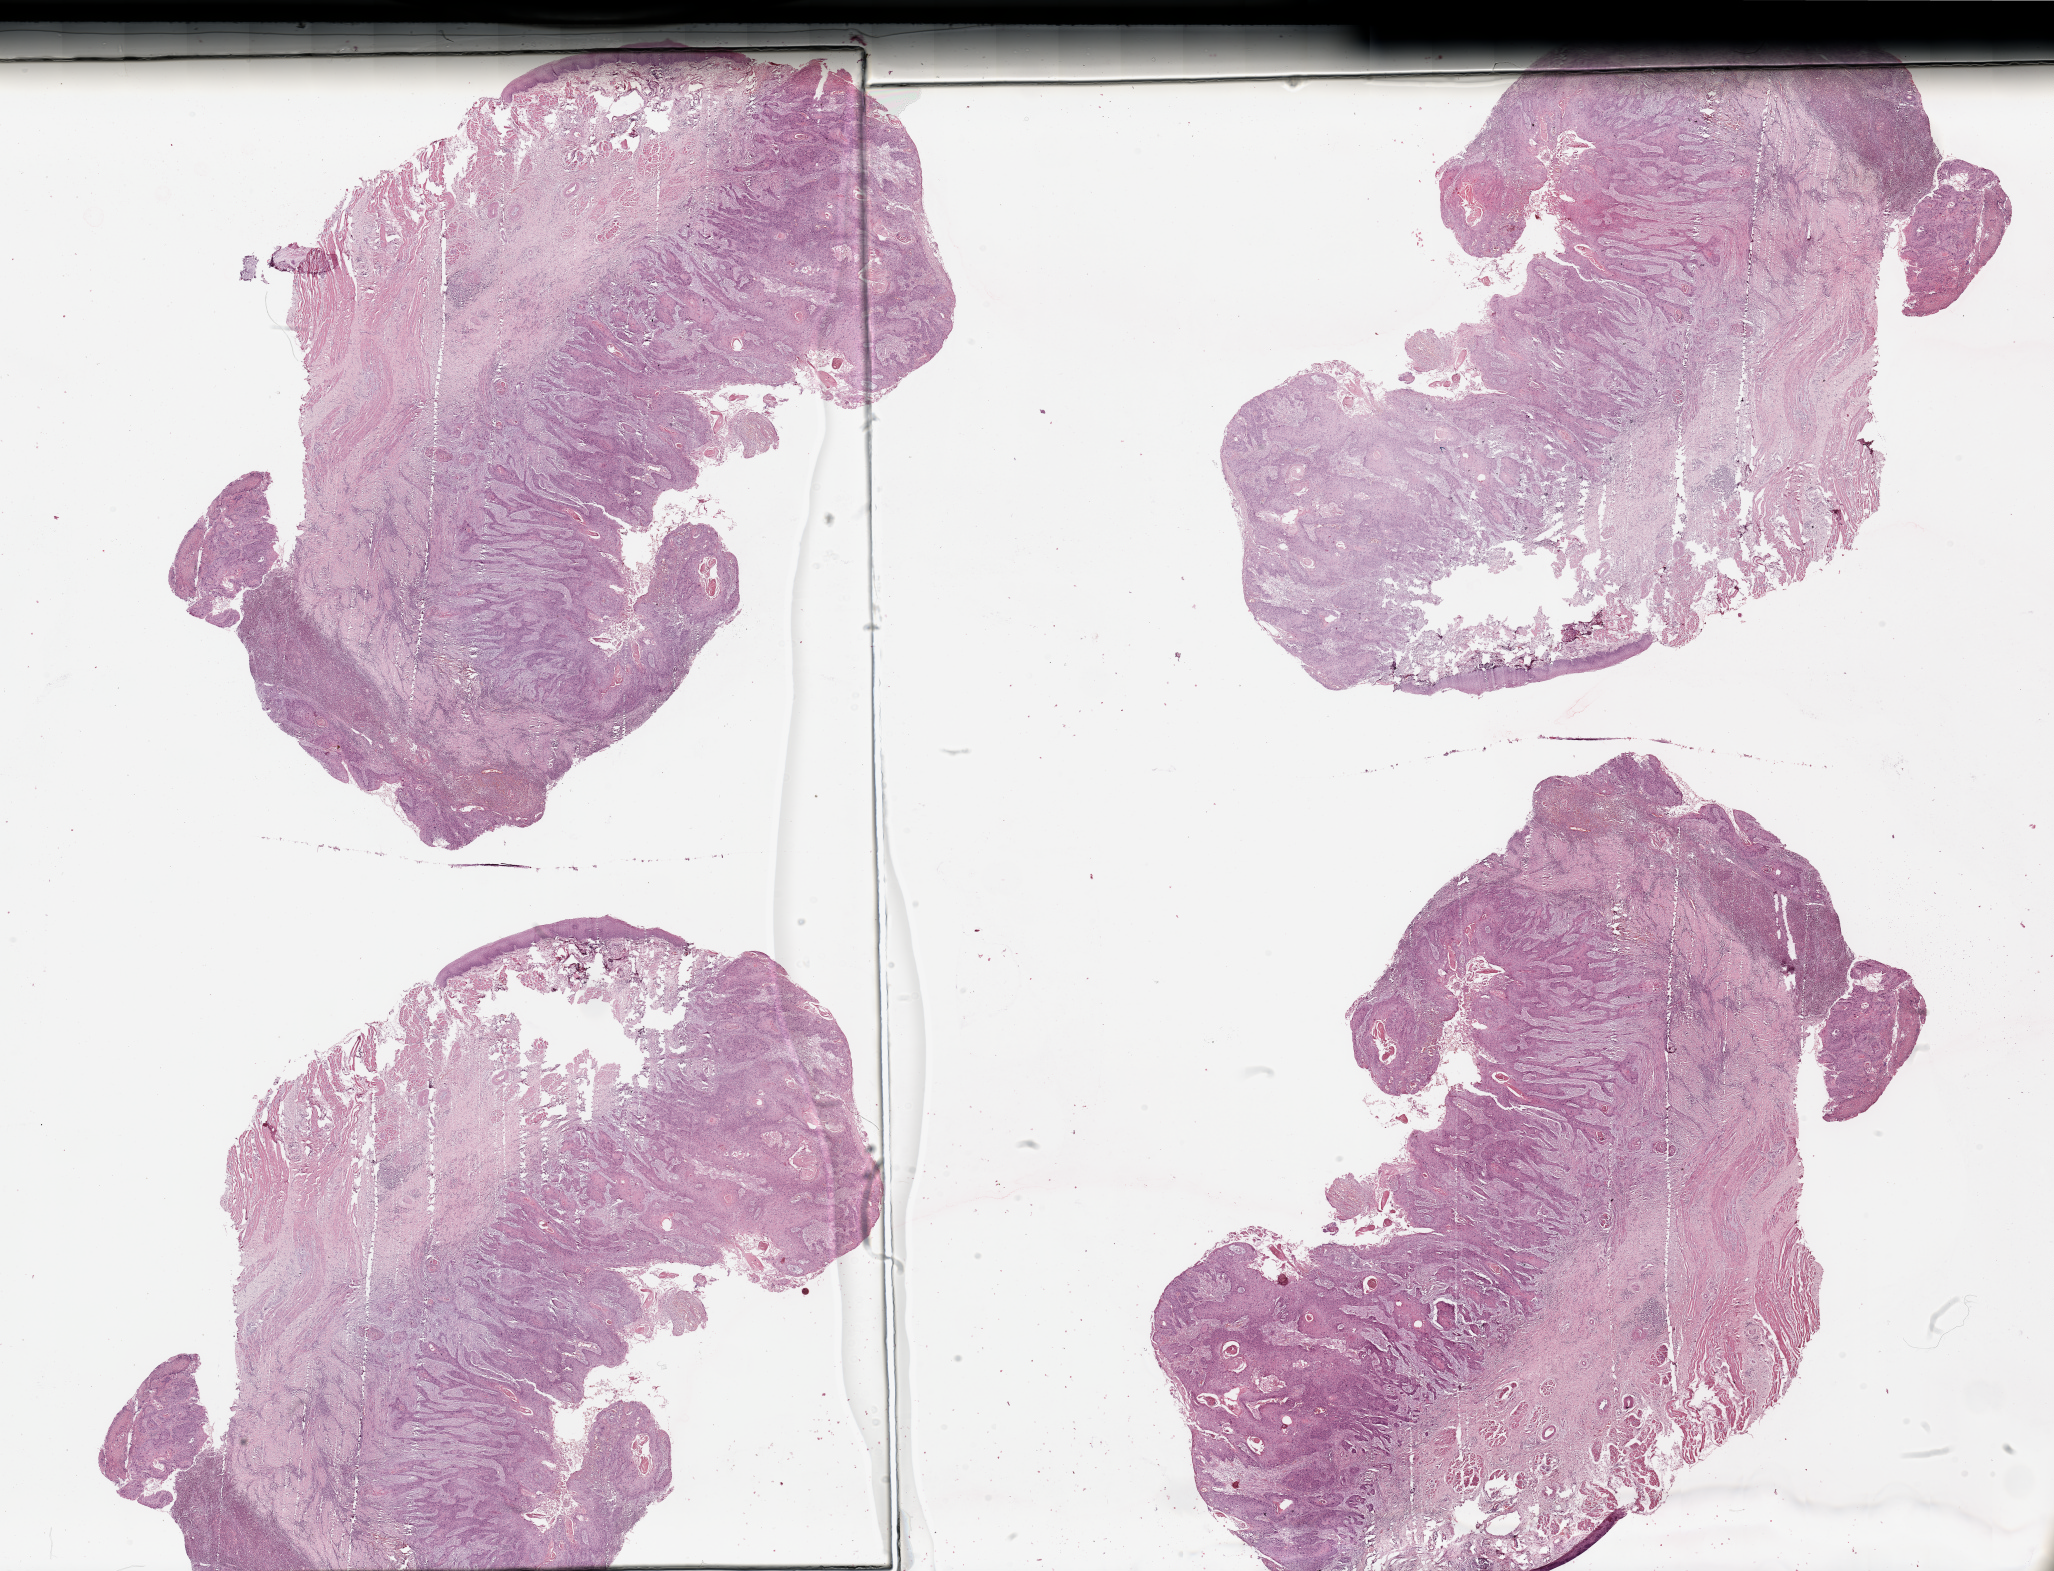
Whole-slide histology image, Hematoxylin and eosin (H&E) stained — a low-resolution overview of the entire scanned area, about 32.5 x 24.8 mm. Head and neck, tissue type not recorded. Male, 64 y/o.
Patient diagnosis: Squamous cell carcinoma, NOS (head, face or neck, NOS).